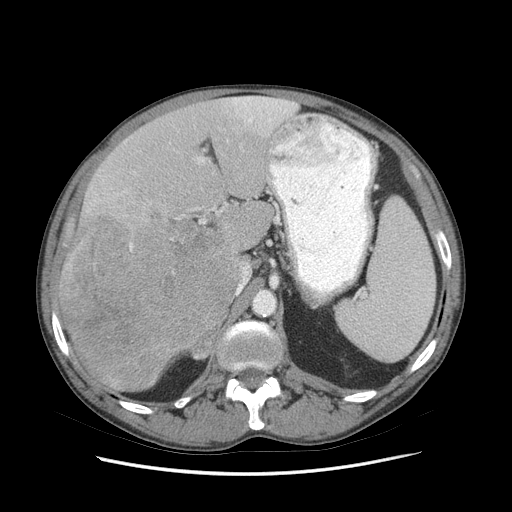
Contrast-enhanced abdominal CT (liver protocol), one axial slice. Slice 48 of 89 in the series (ordered by position). Reconstruction kernel STANDARD. 140 kVp. Soft-tissue window (W 400 / L 40 HU). 512 × 512 image matrix, field of view 380 × 380 mm. From the clinical record (not read from this slice): diagnosis: hepatocellular carcinoma (patient treated with transarterial chemoembolisation; whether this scan precedes or follows treatment is not stated here); TNM stage (as recorded): Stage-IIIB; Child-Pugh class: A; tumour differentiation: moderately differentiated; tumour nodularity: multinodular.
Annotated regions visible in this slice (semi-automatic segmentation, software-assisted and operator-edited):
- liver parenchyma outside the tumour (the mass and vessels are separate outlines, so this box may not span the whole liver): bounding box [x1, y1, x2, y2] px = [56, 96, 296, 392]
- mass: [58, 207, 240, 390]
- liver vessels: [198, 97, 294, 222]